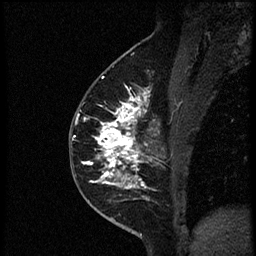
Breast MRI (dynamic contrast-enhanced), one sagittal slice. Position 32 of 56 along the scan axis. Dynamic contrast-enhanced study with each time point stored as its own series, time point 2 of 4 at this slice position (early post-contrast, ordered by acquisition time). 1.5 T. TE 4.2 ms, TR 18.9 ms. 256 × 256 image matrix, field of view 200 × 200 mm. Female patient. From the clinical record (not read from this slice): setting: breast cancer imaged before/during neoadjuvant chemotherapy; receptor status: HER2-positive.
Outlined on this slice (semi-automatic segmentation, software-assisted and operator-edited):
- analysis volume of interest (the breast-tissue region the enhancement analysis was run in; not a lesion): bounding box [x1, y1, x2, y2] px = [78, 86, 174, 189]
- tumour enhancement mask (voxels above the 100 % enhancement threshold inside the analysis volume of interest): [83, 91, 159, 189]